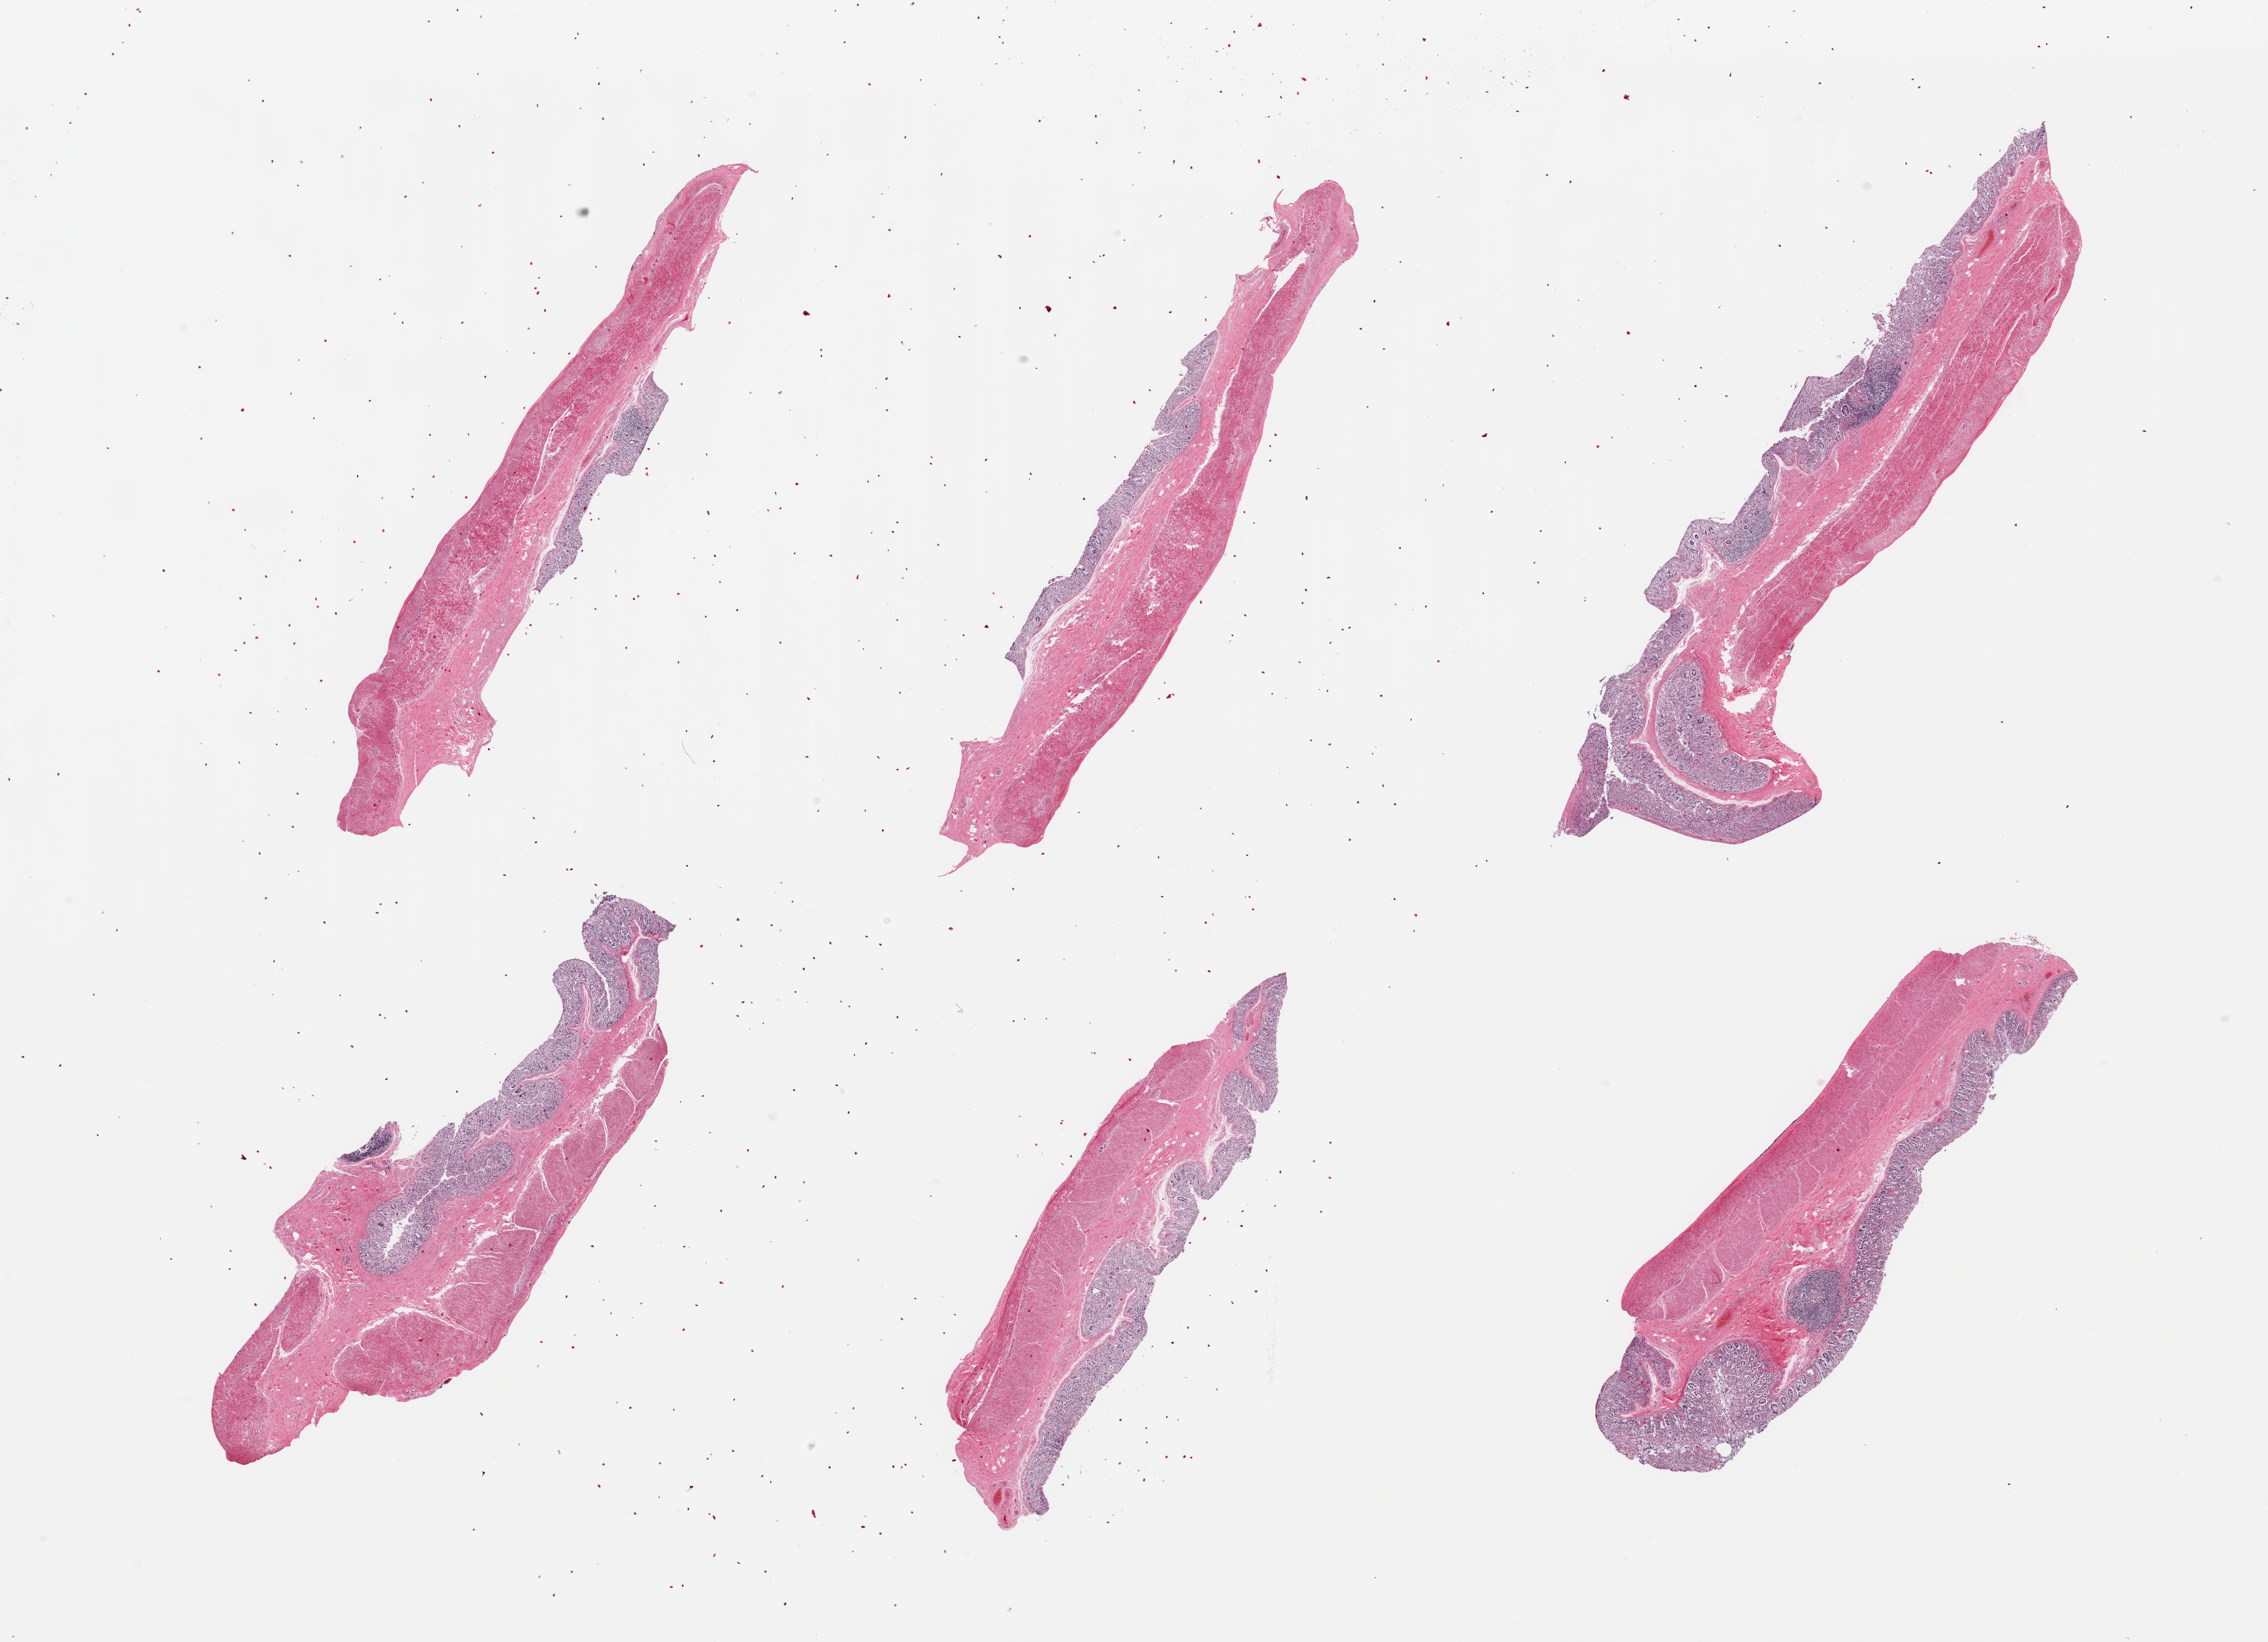
Hematoxylin and eosin (H&E) whole-slide image — low-resolution overview of the scanned area, about 26.6 x 19.2 mm, PAXgene-fixed, paraffin-embedded tissue, sampled site (target tissue): transverse colon, donor tissue sample. Donor: male.
- reviewer comment on this tissue sample: 6 pieces; mucosa severely autolyzed; muscle intact